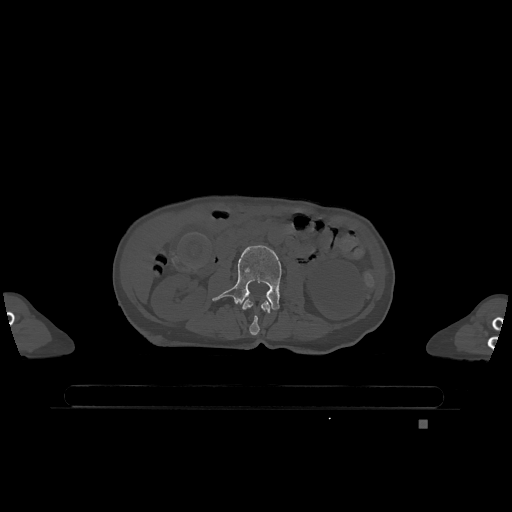
CT including the spine, one axial slice. Position 373 of 1317 along the scan axis. Bone window (W 1800 / L 400 HU). 512 × 512 image matrix, field of view 500 × 500 mm. Female patient, age 74 years. Case-level facts recorded for this patient, not image findings: primary cancer: lung.
Annotated regions visible in this slice (semi-automatic segmentation, software-assisted and operator-edited):
- L2 vertebra: box from (x=242, y=299) to (x=272, y=336) px
- L3 vertebra: (x=212, y=245)–(x=282, y=310)